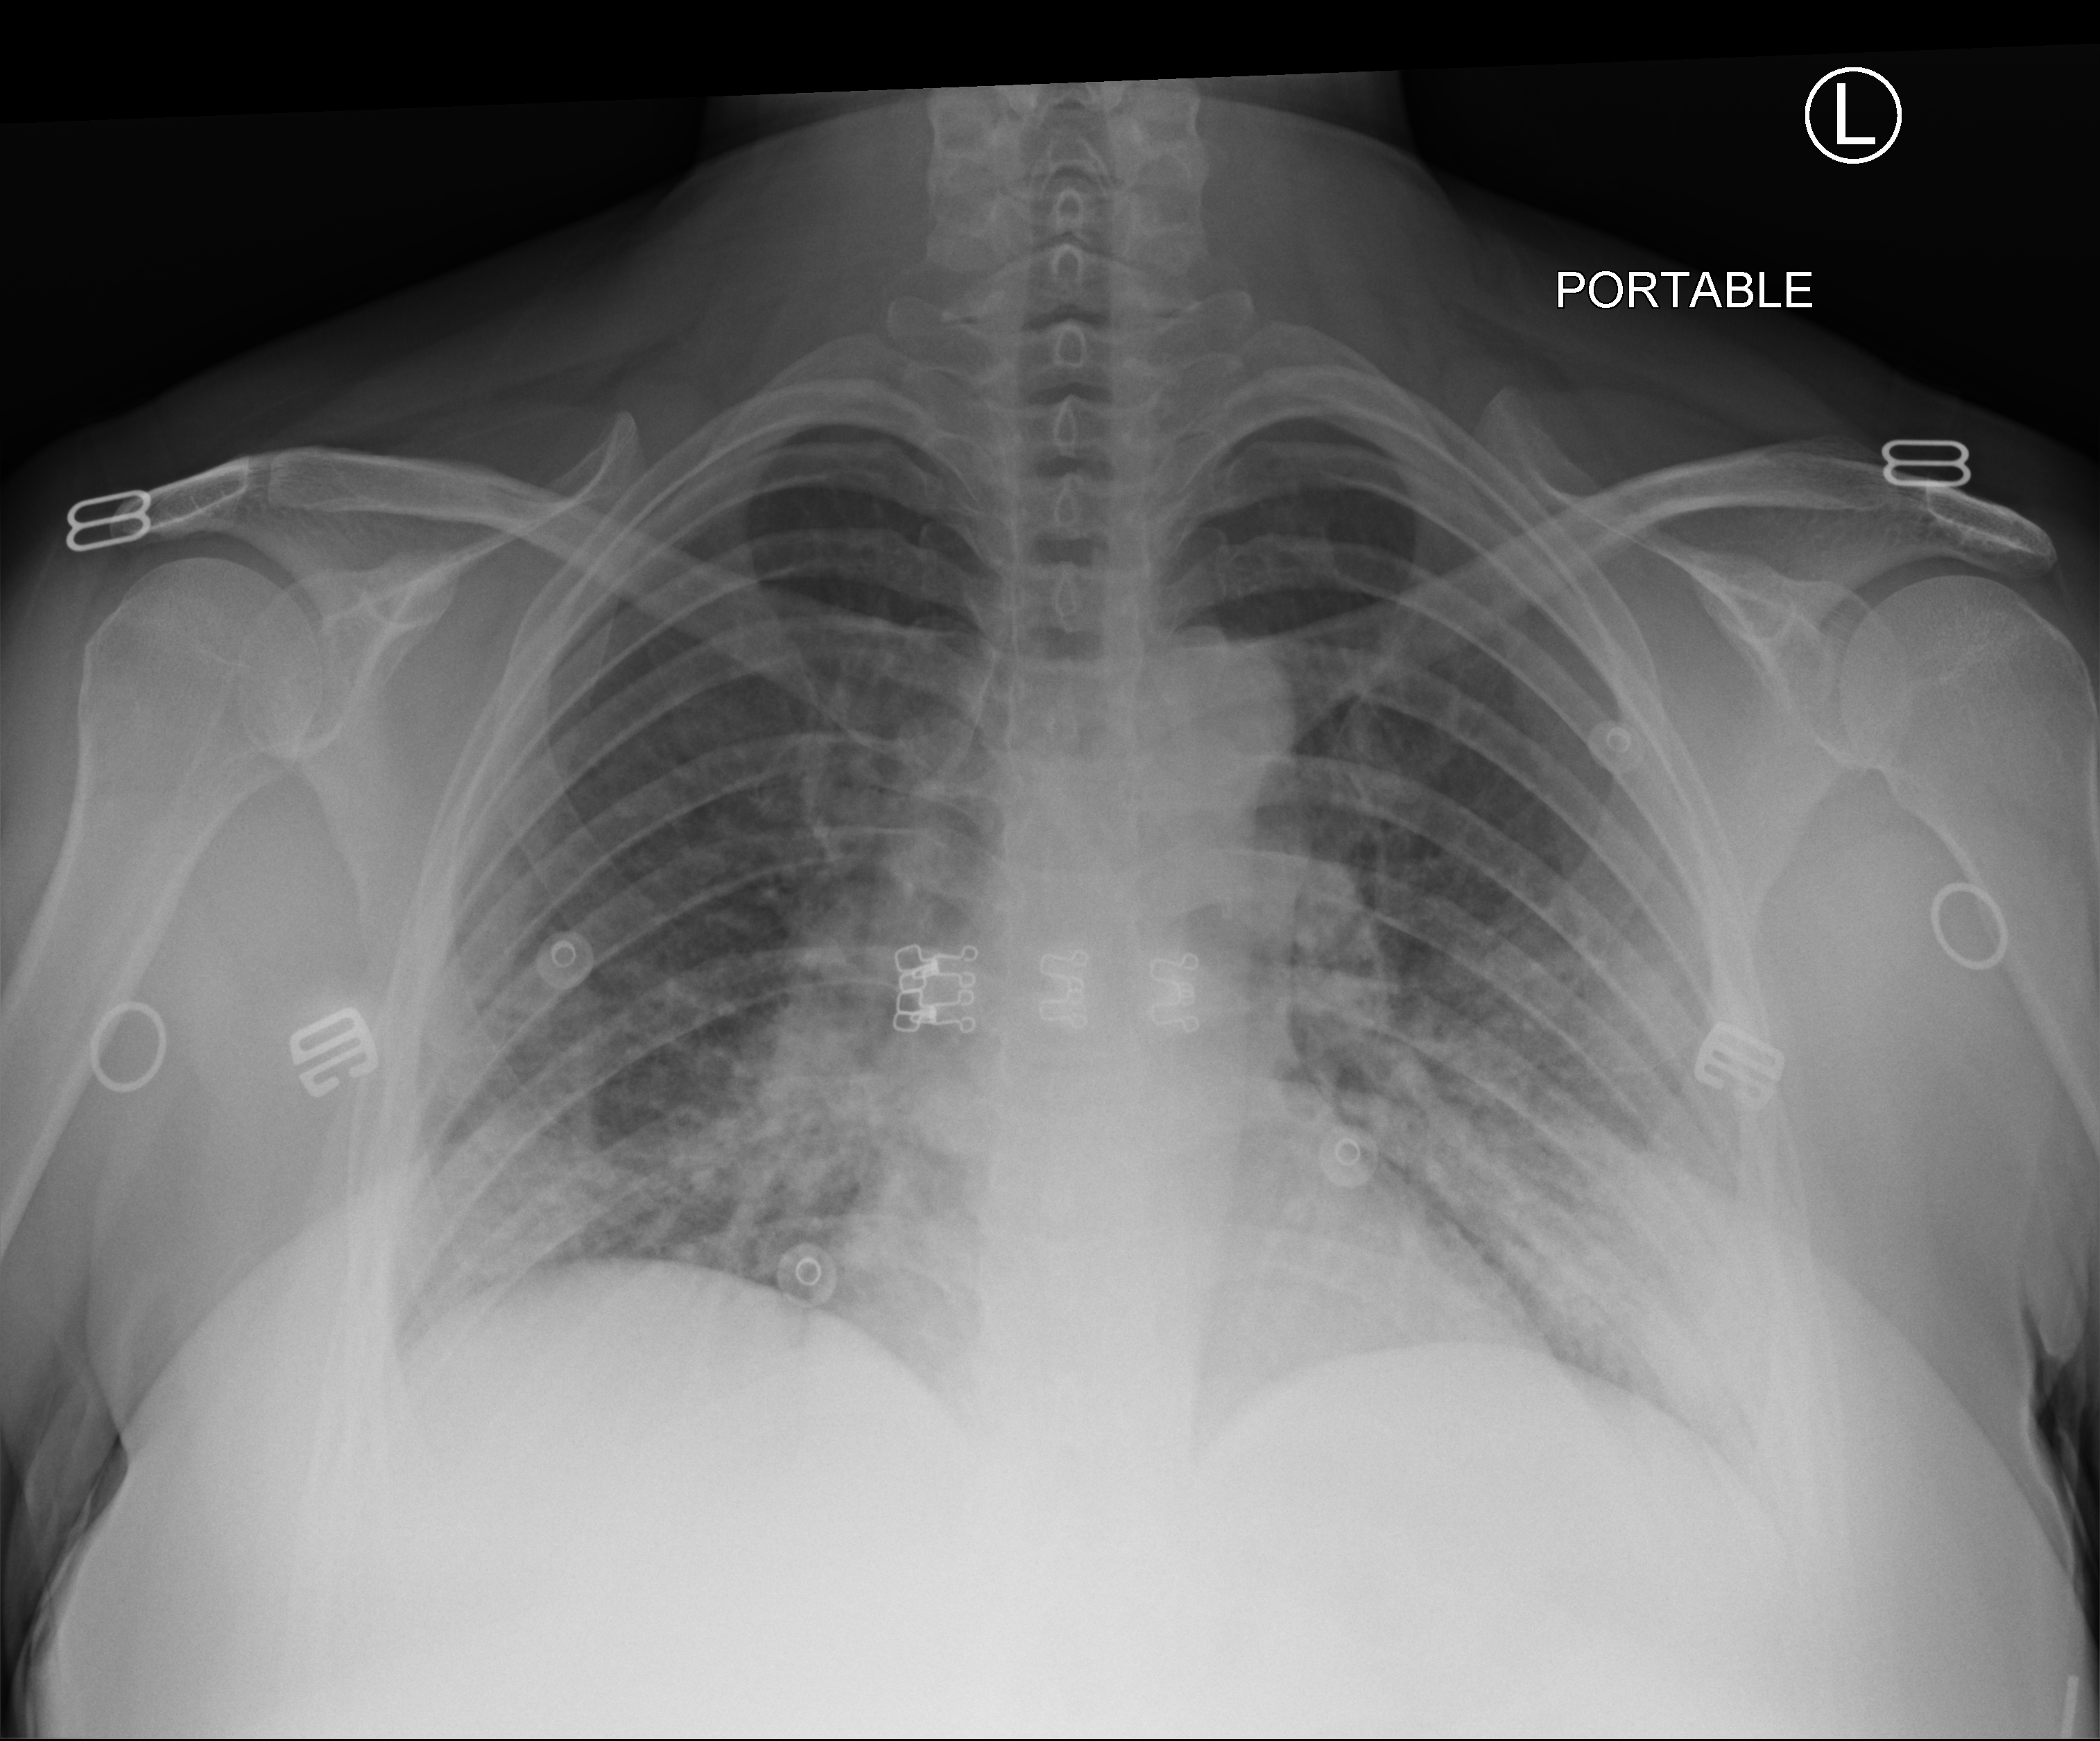
Portable chest radiograph. Patient hospitalised with COVID-19; female, aged 18–59 years.
From the hospital-stay record, not from the radiograph (when in the stay this image was taken is not recorded): diabetes (admission record): no; COPD (admission record): no; hypertension (admission record): yes.